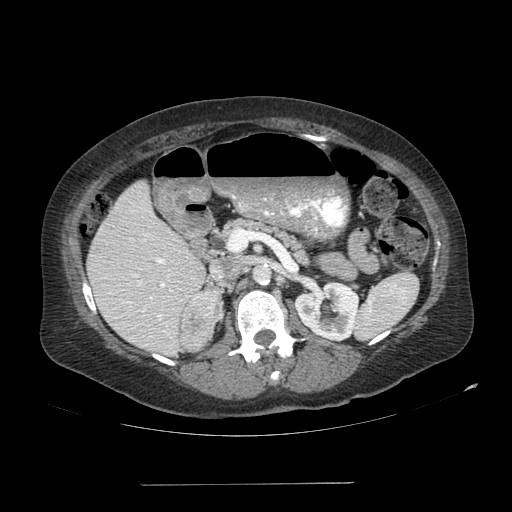
Contrast-enhanced abdominal CT, one axial slice; reconstruction kernel SOFT; 120 kVp; soft-tissue window (W 400 / L 40 HU); 2.5 mm slice thickness; 512 × 512 image matrix, field of view 440 × 440 mm. Female patient, age 67 years. Case-level facts recorded for this patient, not image findings: diagnosis: adrenocortical carcinoma; tumour side: right adrenal; tumour size at pathology: 9.8 cm; Ki-67 index: 59 %.
Annotated regions visible in this slice (semi-automatic segmentation, software-assisted and operator-edited):
- mass: bounding box (x1, y1, x2, y2) in pixels: (181, 294, 219, 350)